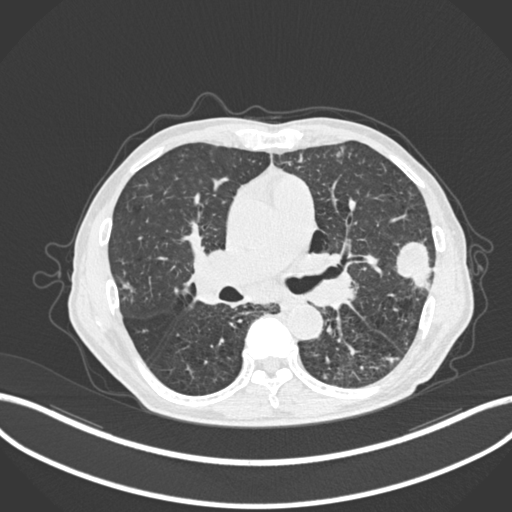
Chest CT, one axial slice; position 134 of 287 along the scan axis; reconstruction kernel B30f; 120 kVp; lung window (W 1500 / L -600 HU); 1 mm slice thickness; 512 × 512 image matrix. Patient: male, 74 years. From the clinical record (not read from this slice): clinical TNM (as recorded): T2a N1 M0.
Structures marked on this image (bounding box drawn by a radiologist):
- lung tumour (recorded histology: adenocarcinoma): box from (x=394, y=239) to (x=435, y=292) px